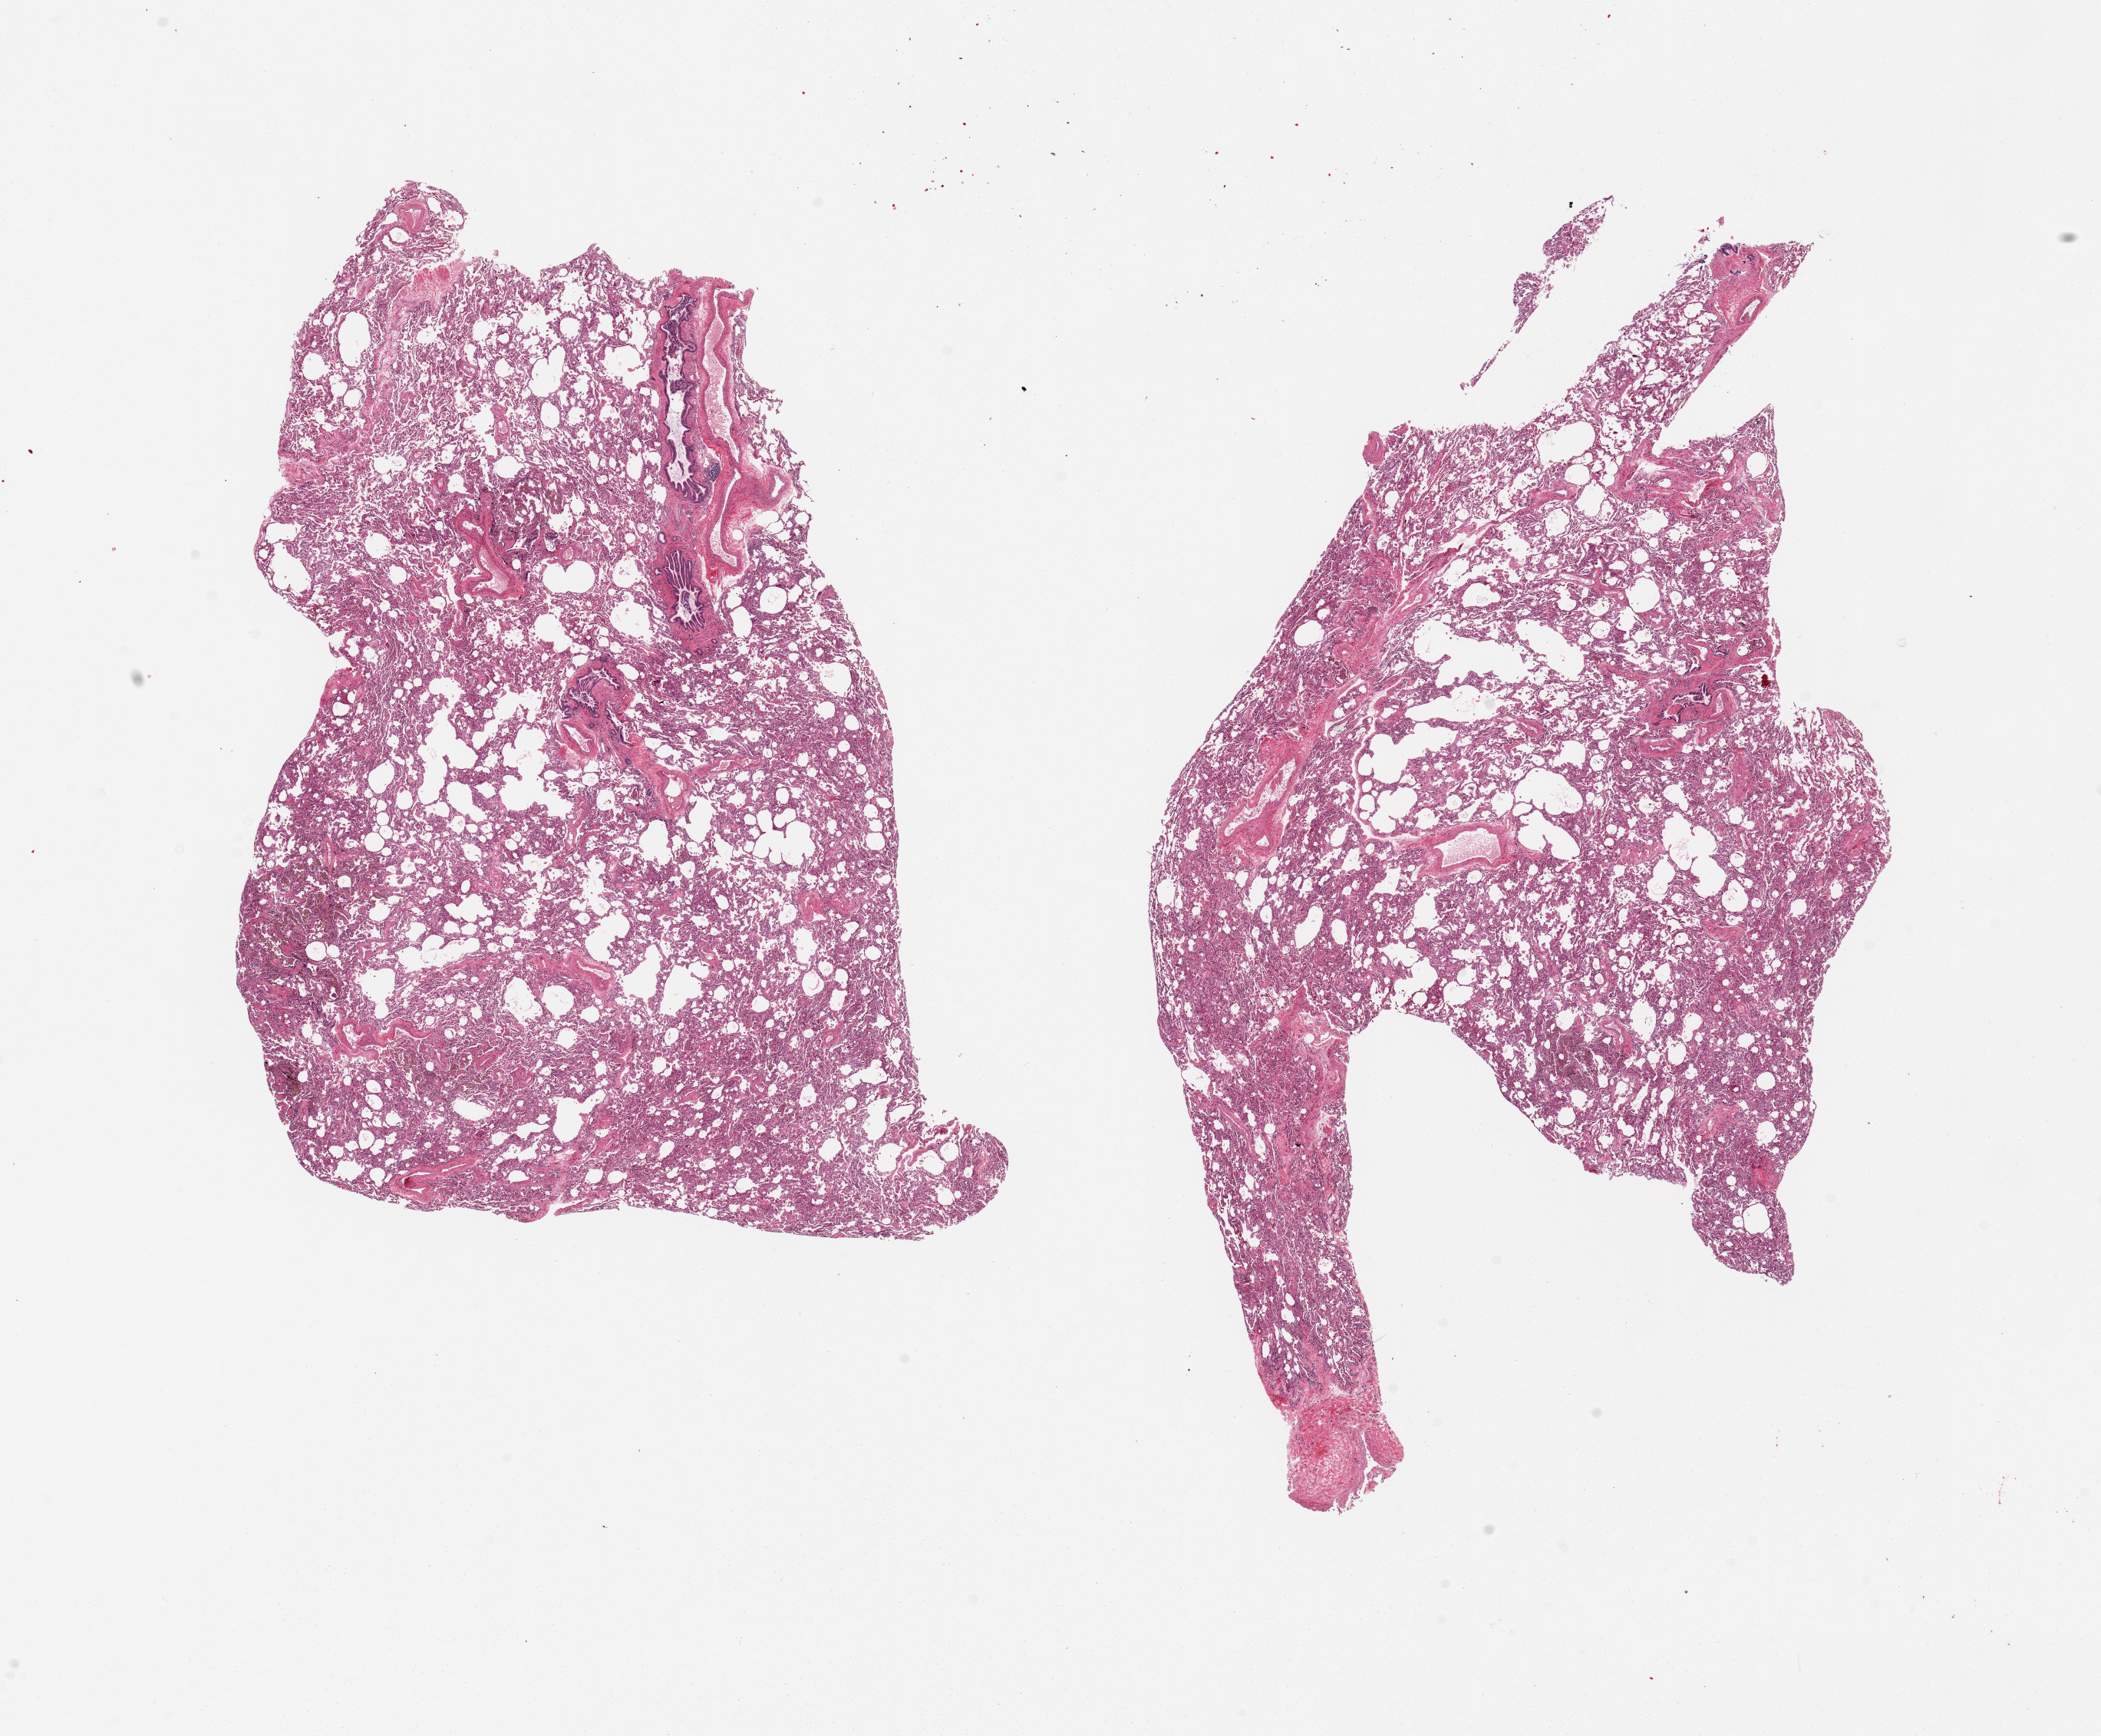
Digitized H&E-stained section, a low-resolution overview of the entire scanned area, about 21.7 x 17.9 mm, PAXgene-fixed paraffin-embedded (PFPE) section, section of lung (target tissue), donor tissue sample. Donor sex: male.
Reviewer comment on this tissue sample: 2 pieces, 10x7.5 and 11x8mm; 1 mm fibrous area.